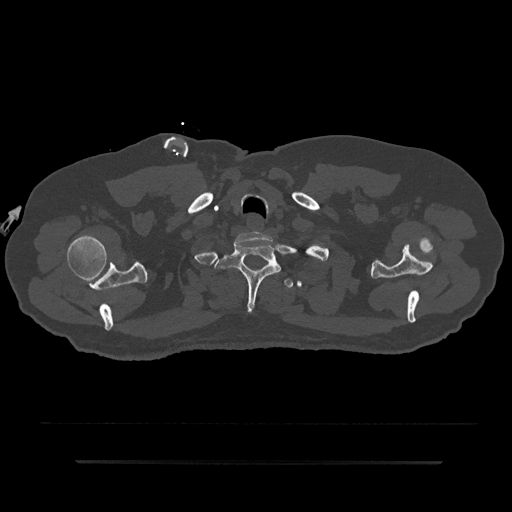
CT including the spine, one axial slice. Position 737 of 797 along the scan axis. Reconstruction kernel Br40s/3. 120 kVp. Bone window (W 1800 / L 400 HU). 512 × 512 image matrix. Male patient, age 59 years. From the clinical record (not read from this slice): primary cancer: bile ducts.
Structures marked on this image (semi-automatically segmented with operator editing):
- T1 vertebra: box from (x=214, y=239) to (x=281, y=312) px
- T2 vertebra: (x=284, y=278)–(x=294, y=288)